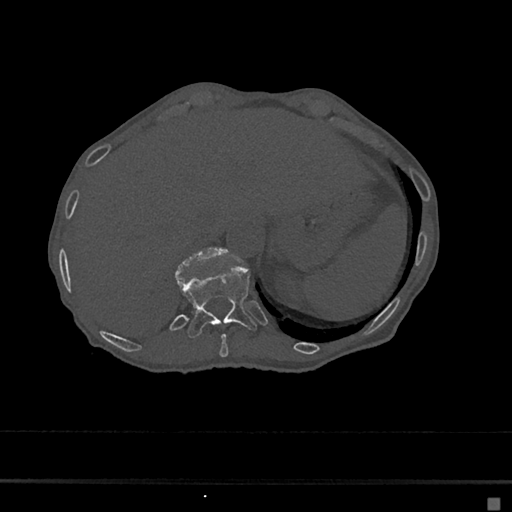
CT including the spine, one axial slice. Slice 179 of 797 in the series (ordered by position). Reconstruction kernel Br40s/3. Bone window (W 1800 / L 400 HU). 0.5 mm slice thickness. 512 × 512 image matrix. Female patient, age 68 years. Case-level facts recorded for this patient, not image findings: primary cancer: renal.
Outlined on this slice (semi-automatic segmentation, software-assisted and operator-edited):
- T10 vertebra: bounding box (x1, y1, x2, y2) in pixels: (219, 334, 228, 358)
- T11 vertebra: (176, 265, 257, 339)
- T12 vertebra: (178, 247, 226, 270)